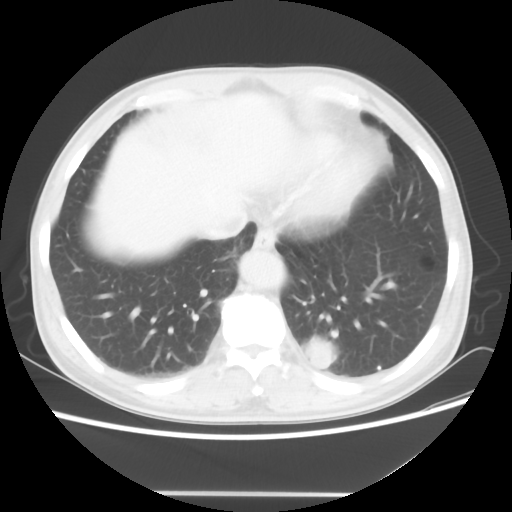
Chest CT, one axial slice; position 14 of 60 along the scan axis; 100 kVp; lung window (W 1500 / L -600 HU); 5 mm slice thickness; 512 × 512 image matrix. Patient: male, 55 years. From the clinical record (not read from this slice): clinical TNM (as recorded): T1c N3 M0; histopathological grade: G3.
Annotated regions visible in this slice (rectangle marked by the reading radiologist):
- lung tumour (recorded histology: small cell carcinoma): bounding box <298,329,337,376> (left, top, right, bottom; pixels)